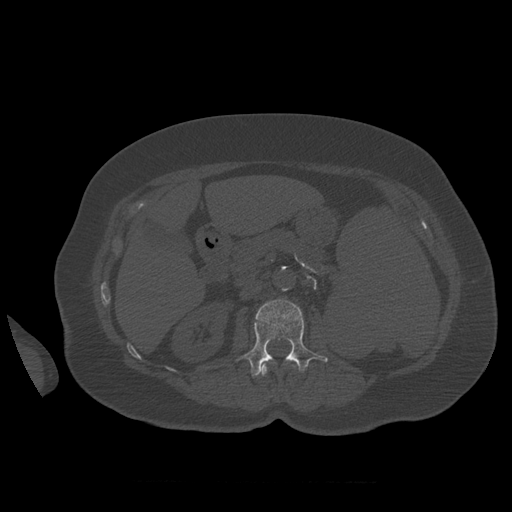
CT including the spine, one axial slice; position 258 of 399 along the scan axis; reconstruction kernel STANDARD; bone window (W 1800 / L 400 HU); 1.25 mm slice thickness; 512 × 512 image matrix. Patient age 81 years. From the clinical record (not read from this slice): primary cancer: renal; vertebrae with lytic lesions (as recorded): L1.
Structures marked on this image (semi-automatically segmented with operator editing):
- L1 vertebra: bounding box [x1, y1, x2, y2] px = [260, 363, 295, 376]
- L2 vertebra: [237, 300, 328, 376]